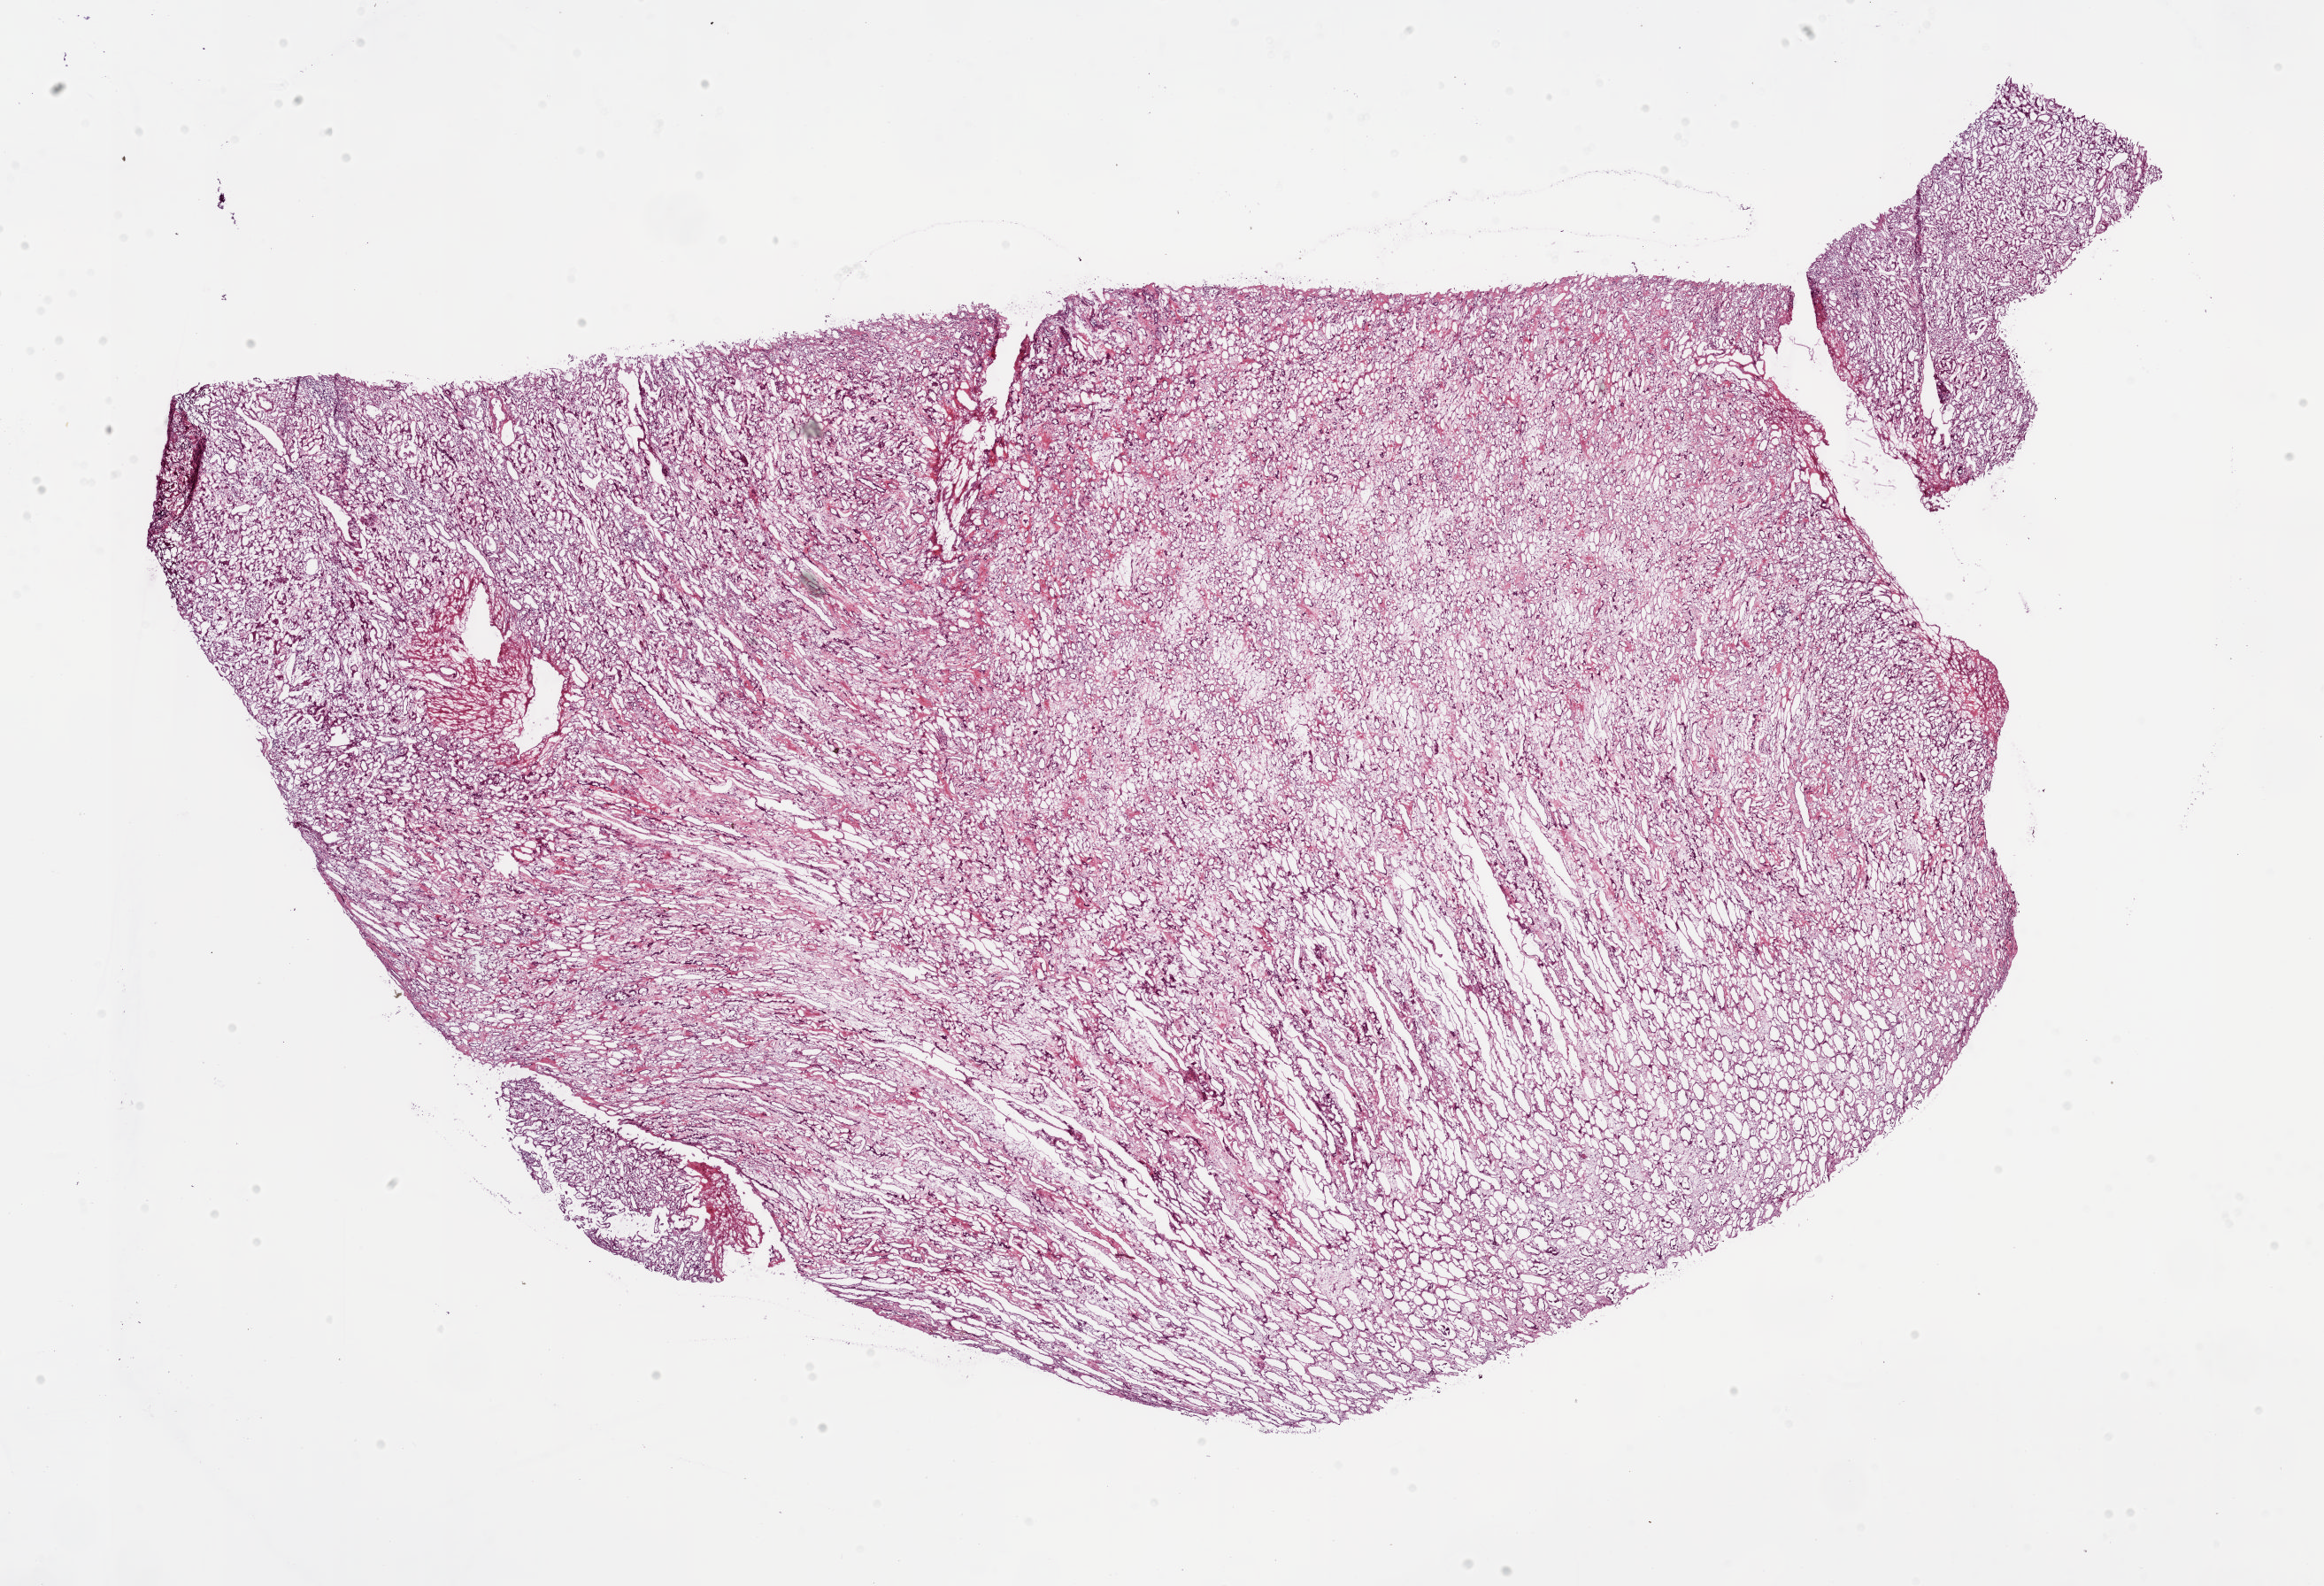
H&E whole-slide image, whole scanned area (about 20.8 x 14.2 mm) shown as a low-resolution overview. Frozen section. Solid tissue normal (non-tumour tissue) sample from the kidney. Male patient; age at initial diagnosis 76 years.
• this section: solid tissue normal sample (biorepository sample class)
• patient diagnosis: Clear cell adenocarcinoma, NOS